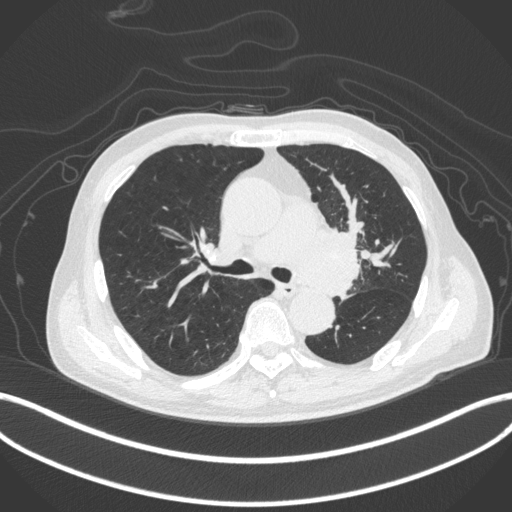
Chest CT, one axial slice; slice 272 of 420 in the series (ordered by position); 120 kVp; lung window (W 1500 / L -600 HU); 1 mm slice thickness; 512 × 512 image matrix, field of view 400 × 400 mm. Male patient, age 77 years. Case-level facts recorded for this patient, not image findings: clinical TNM (as recorded): T3 N1 M0.
Structures marked on this image (rectangle marked by the reading radiologist):
- lung tumour (recorded histology: adenocarcinoma): bounding box [x1, y1, x2, y2] px = [299, 223, 362, 300]